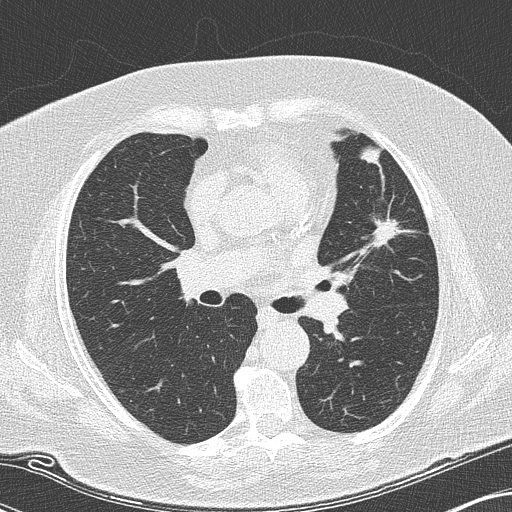
Axial slice from a low-dose chest CT screening exam; second annual screen; lung window (W 1500 / L -600 HU); 2 mm slice thickness; 512 × 512 image matrix. Female, age 73 years at enrolment. Current smoker at enrolment.
Lesion marked by an expert reader, box from (x=366, y=211) to (x=405, y=252) px. The screening reader recorded 2 non-calcified nodules or masses ≥4 mm on this exam; which of them this box marks is not recorded. Official screen result: positive, other. Lung cancer was diagnosed 123 days after this screen: adenocarcinoma, NOS, left upper lobe, moderately differentiated (G2), stage IIIB (AJCC 6th edition), 12 mm at pathology.